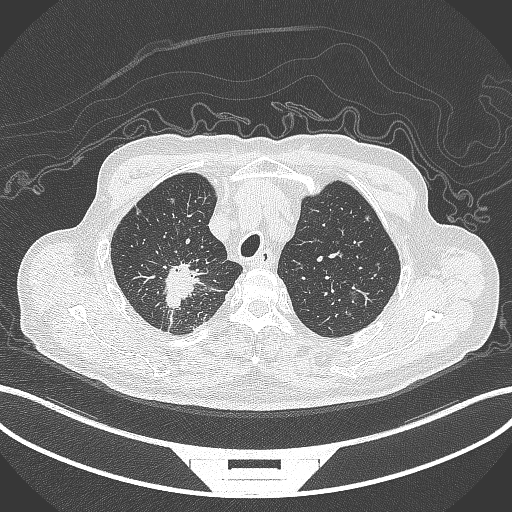
Chest CT, one axial slice. Position 310 of 407 along the scan axis. Reconstruction kernel B70f. Lung window (W 1500 / L -600 HU). 1 mm slice thickness. 512 × 512 image matrix. Male patient, age 69 years. Case-level facts recorded for this patient, not image findings: clinical TNM (as recorded): T1c N1 M1.
Annotated regions visible in this slice (rectangle marked by the reading radiologist):
- lung tumour (recorded histology: adenocarcinoma): bounding box (x1, y1, x2, y2) in pixels: (158, 261, 209, 314)